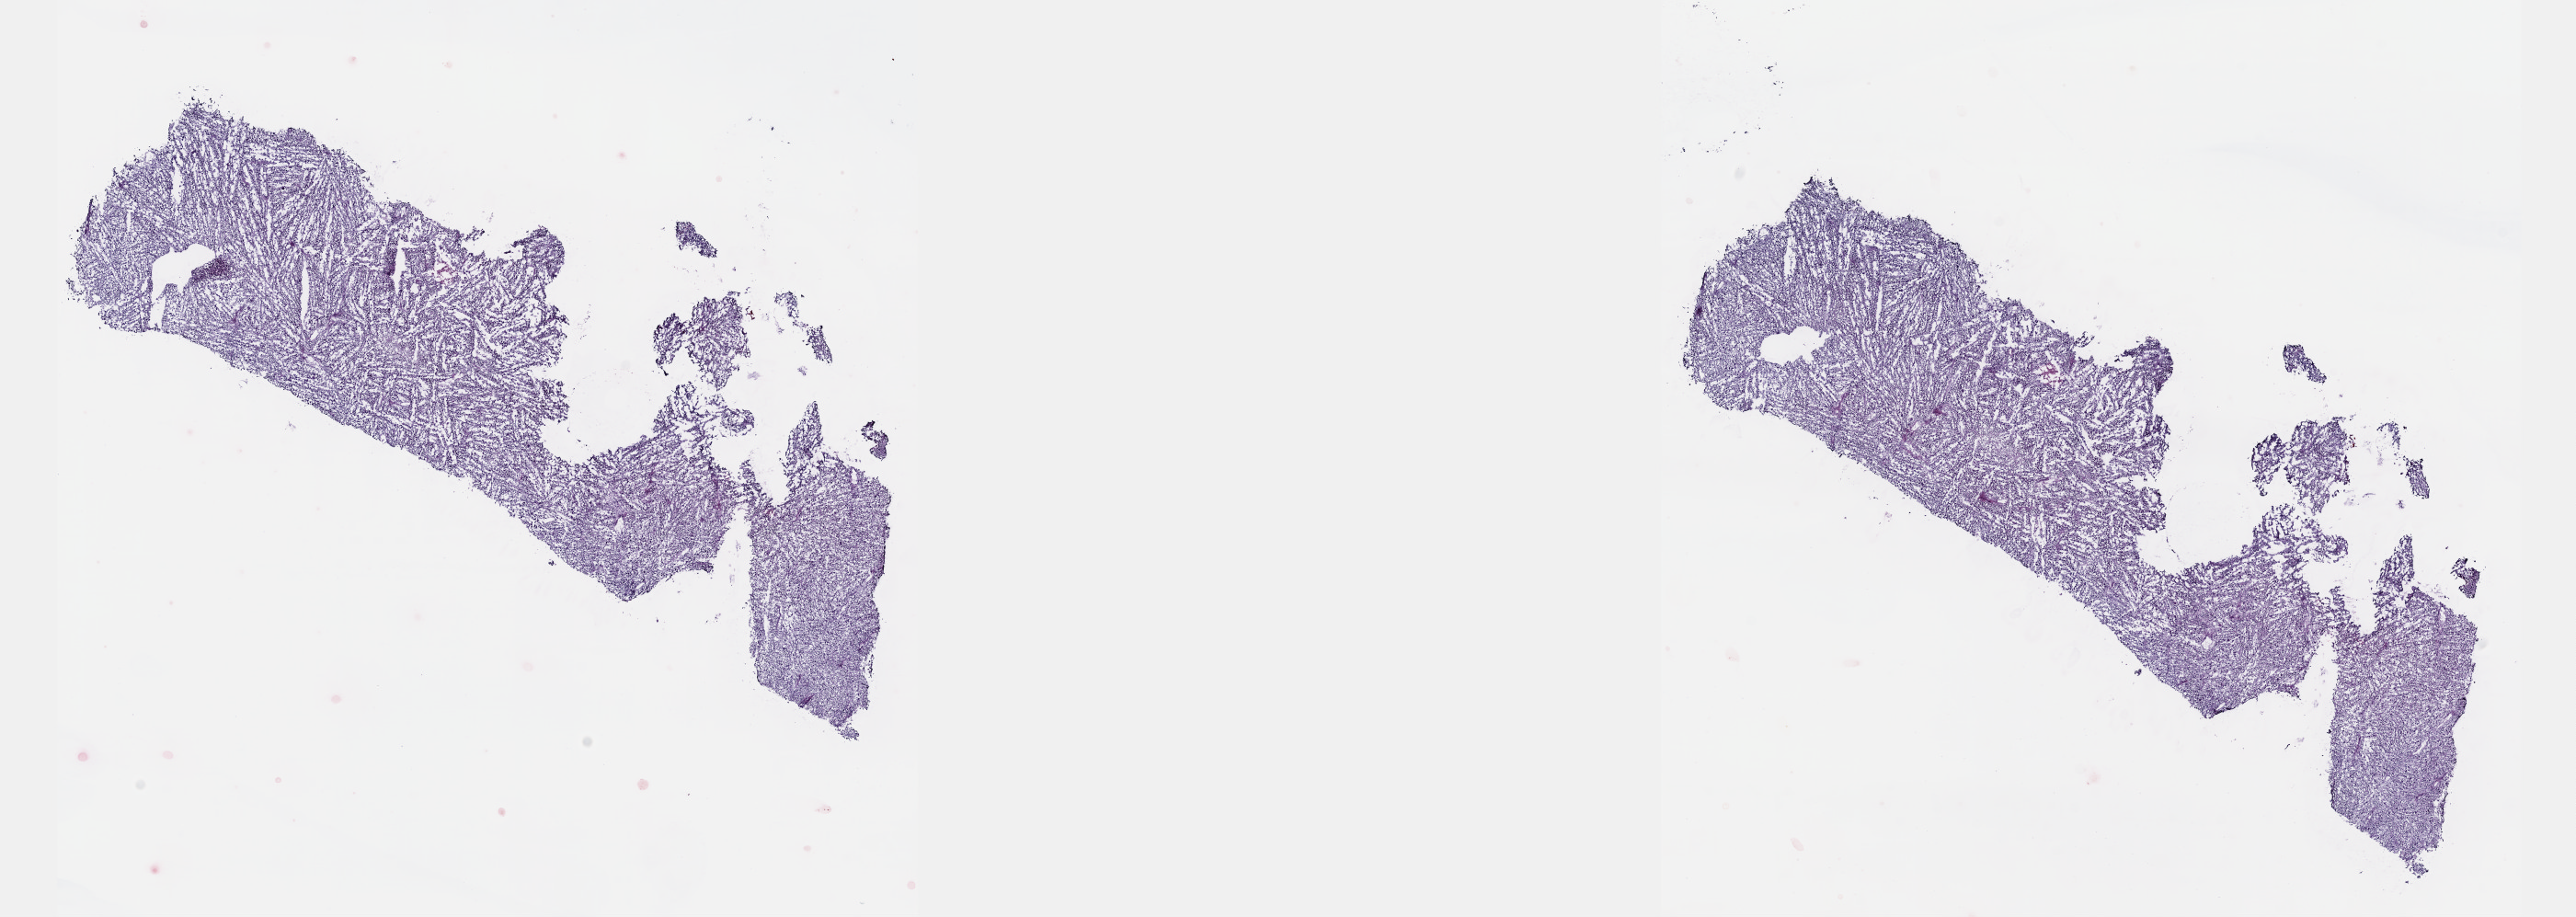
Digitized Hematoxylin and eosin (H&E) stained tissue section (whole slide) — whole scanned area (about 22.6 x 8.1 mm, acquisition: 40x scan) shown as a low-resolution overview, frozen section, primary tumour sample from the connective, subcutaneous and other soft tissues. Male, age 52 years at initial diagnosis. Slide review estimates, as recorded: tumour cells 90%, tumour nuclei 100%, normal cells 0%, stromal cells 8%, necrosis 2%. Infiltration values recorded for this section: lymphocyte infiltration 0%, monocyte infiltration 0%, neutrophil infiltration 0%.
• pathologic diagnosis: Malignant peripheral nerve sheath tumor (connective, subcutaneous and other soft tissues of head, face, and neck)